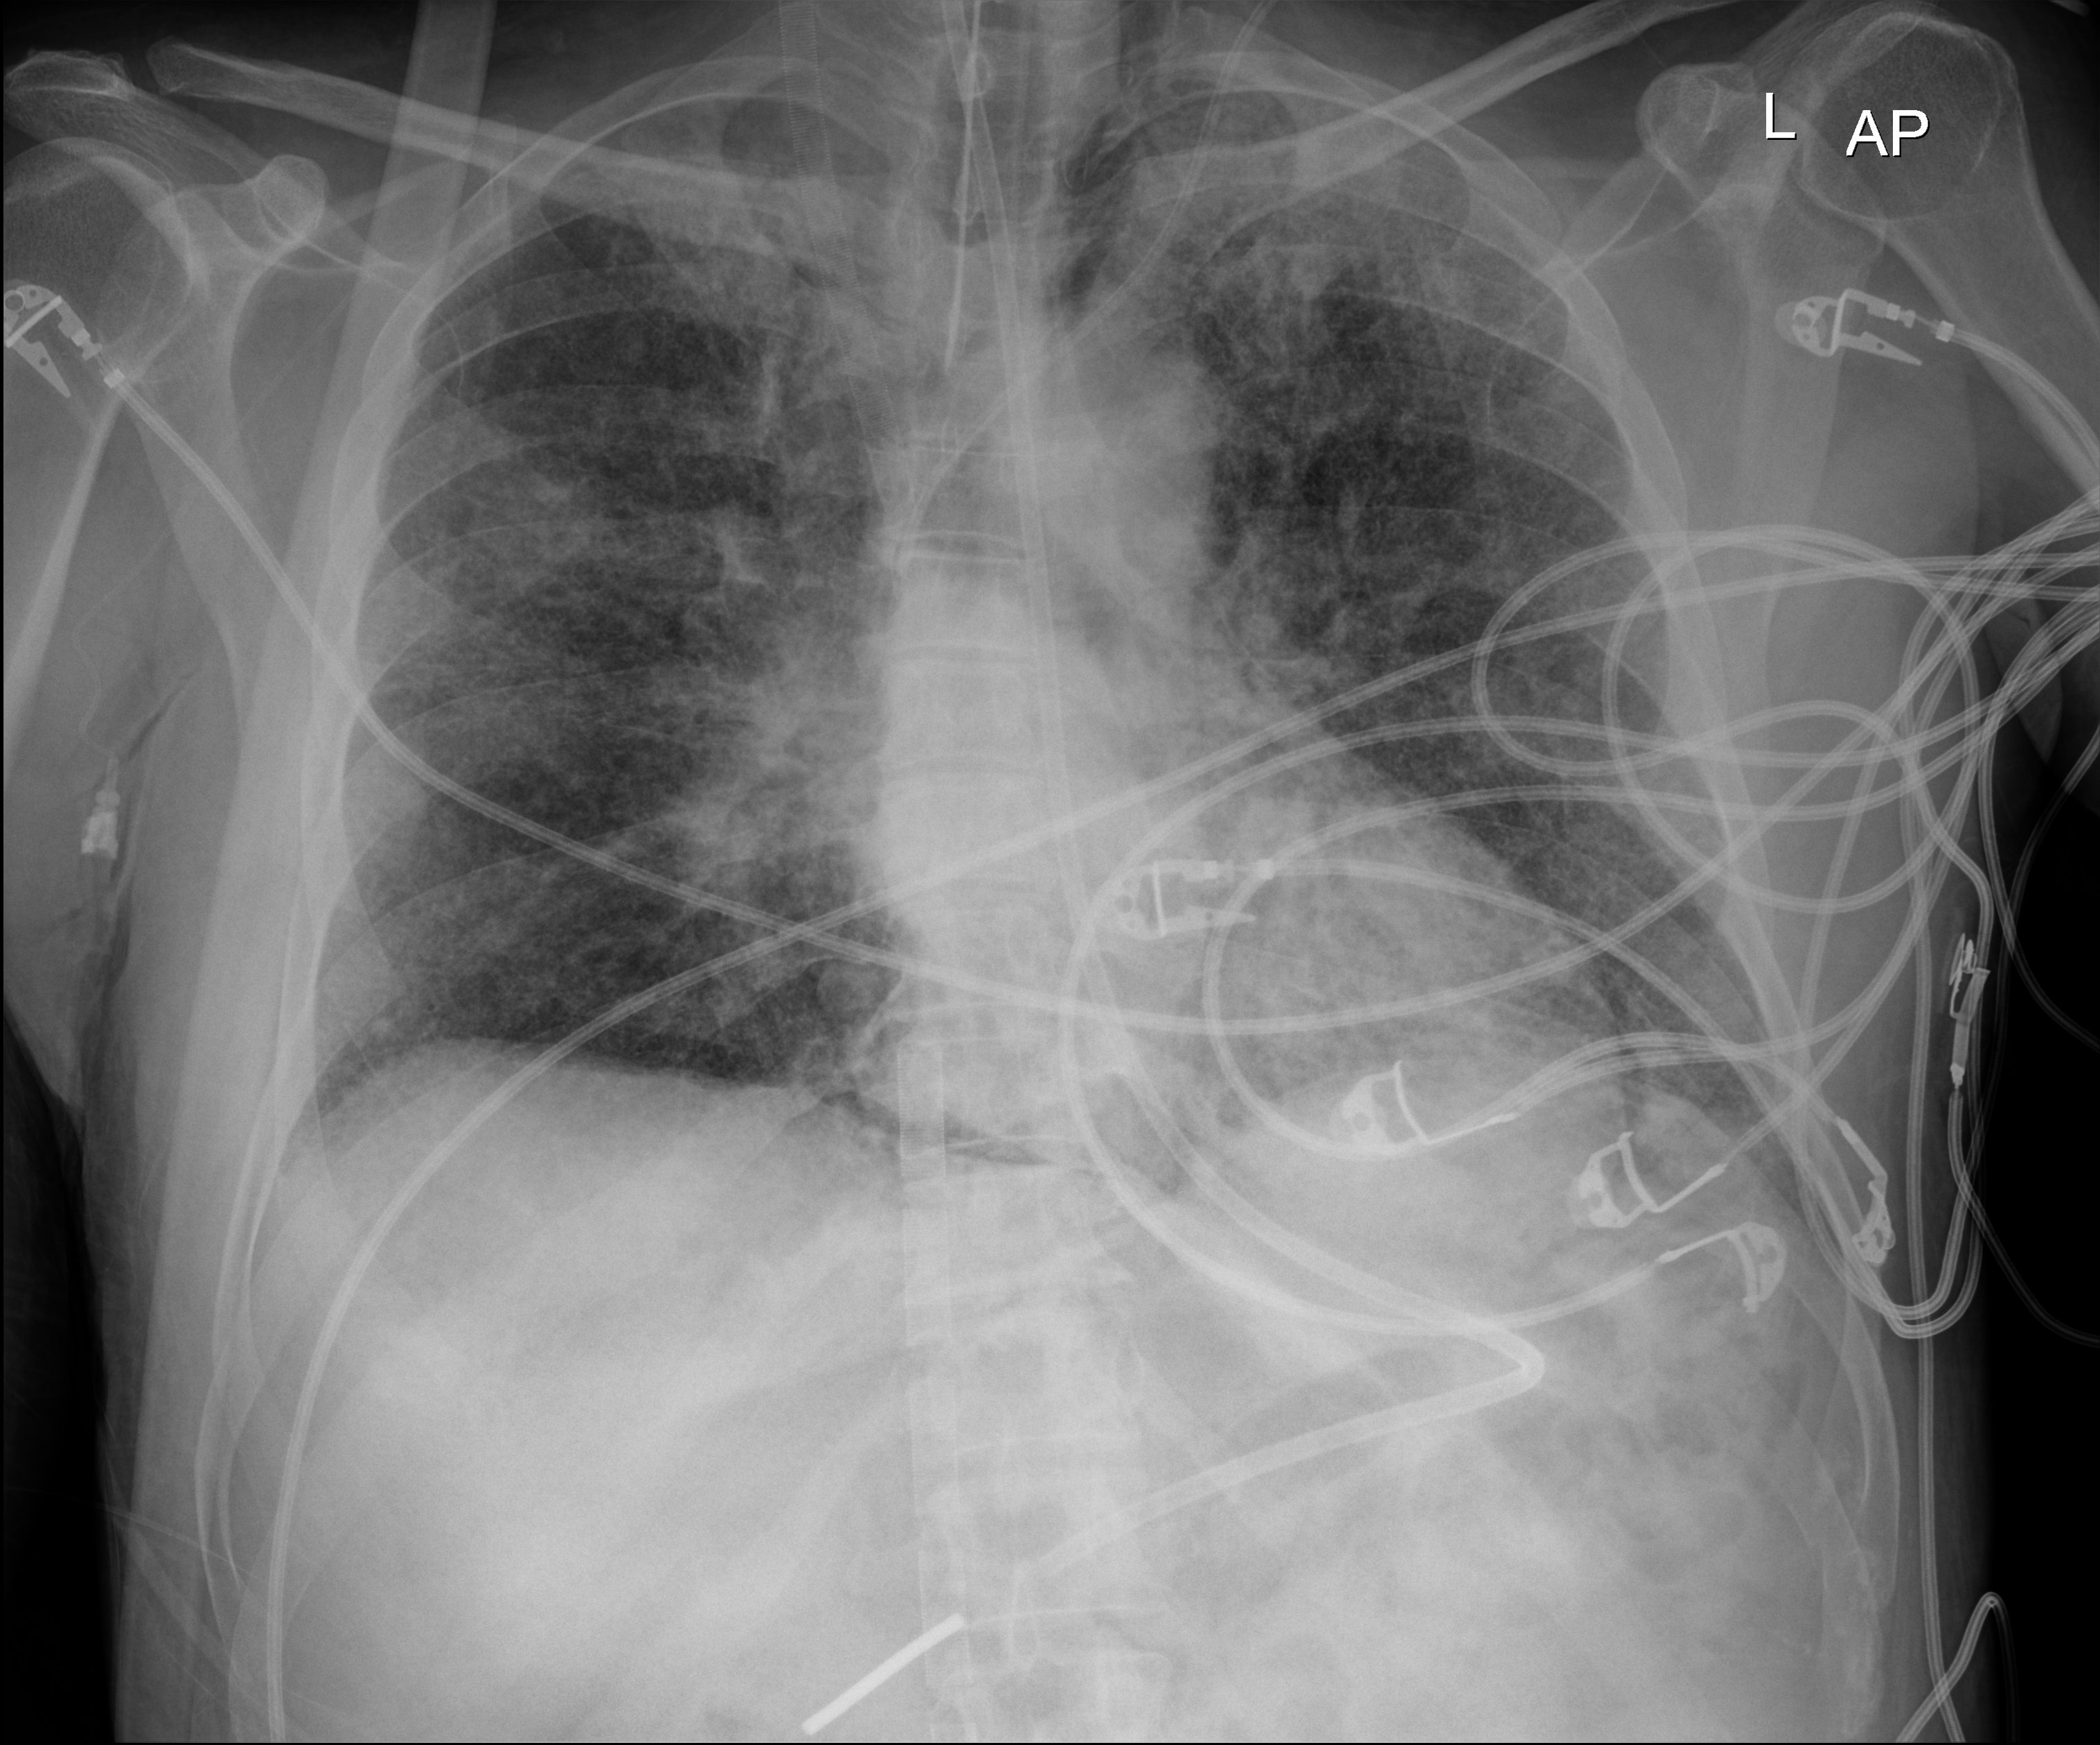
Chest radiograph; anteroposterior (AP) projection. Male patient hospitalised with COVID-19, age 18–59 years.
From the hospital-stay record, not from the radiograph (when in the stay this image was taken is not recorded): admitted to intensive care during this hospital stay: yes; mechanically ventilated during this hospital stay: yes.